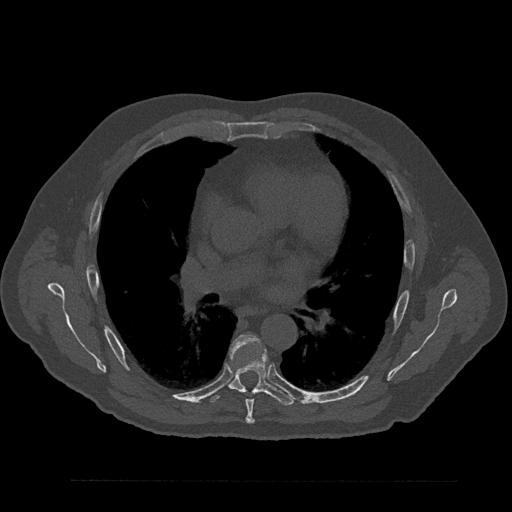
CT including the spine, one axial slice. Slice 528 of 797 in the series (ordered by position). 120 kVp. Bone window (W 1800 / L 400 HU). 0.5 mm slice thickness. 512 × 512 image matrix. Male patient, age 61 years. From the clinical record (not read from this slice): primary cancer: prostate.
Outlined on this slice (semi-automatically segmented with operator editing):
- T6 vertebra: bounding box [x1, y1, x2, y2] px = [230, 335, 260, 424]
- T7 vertebra: [209, 348, 294, 406]